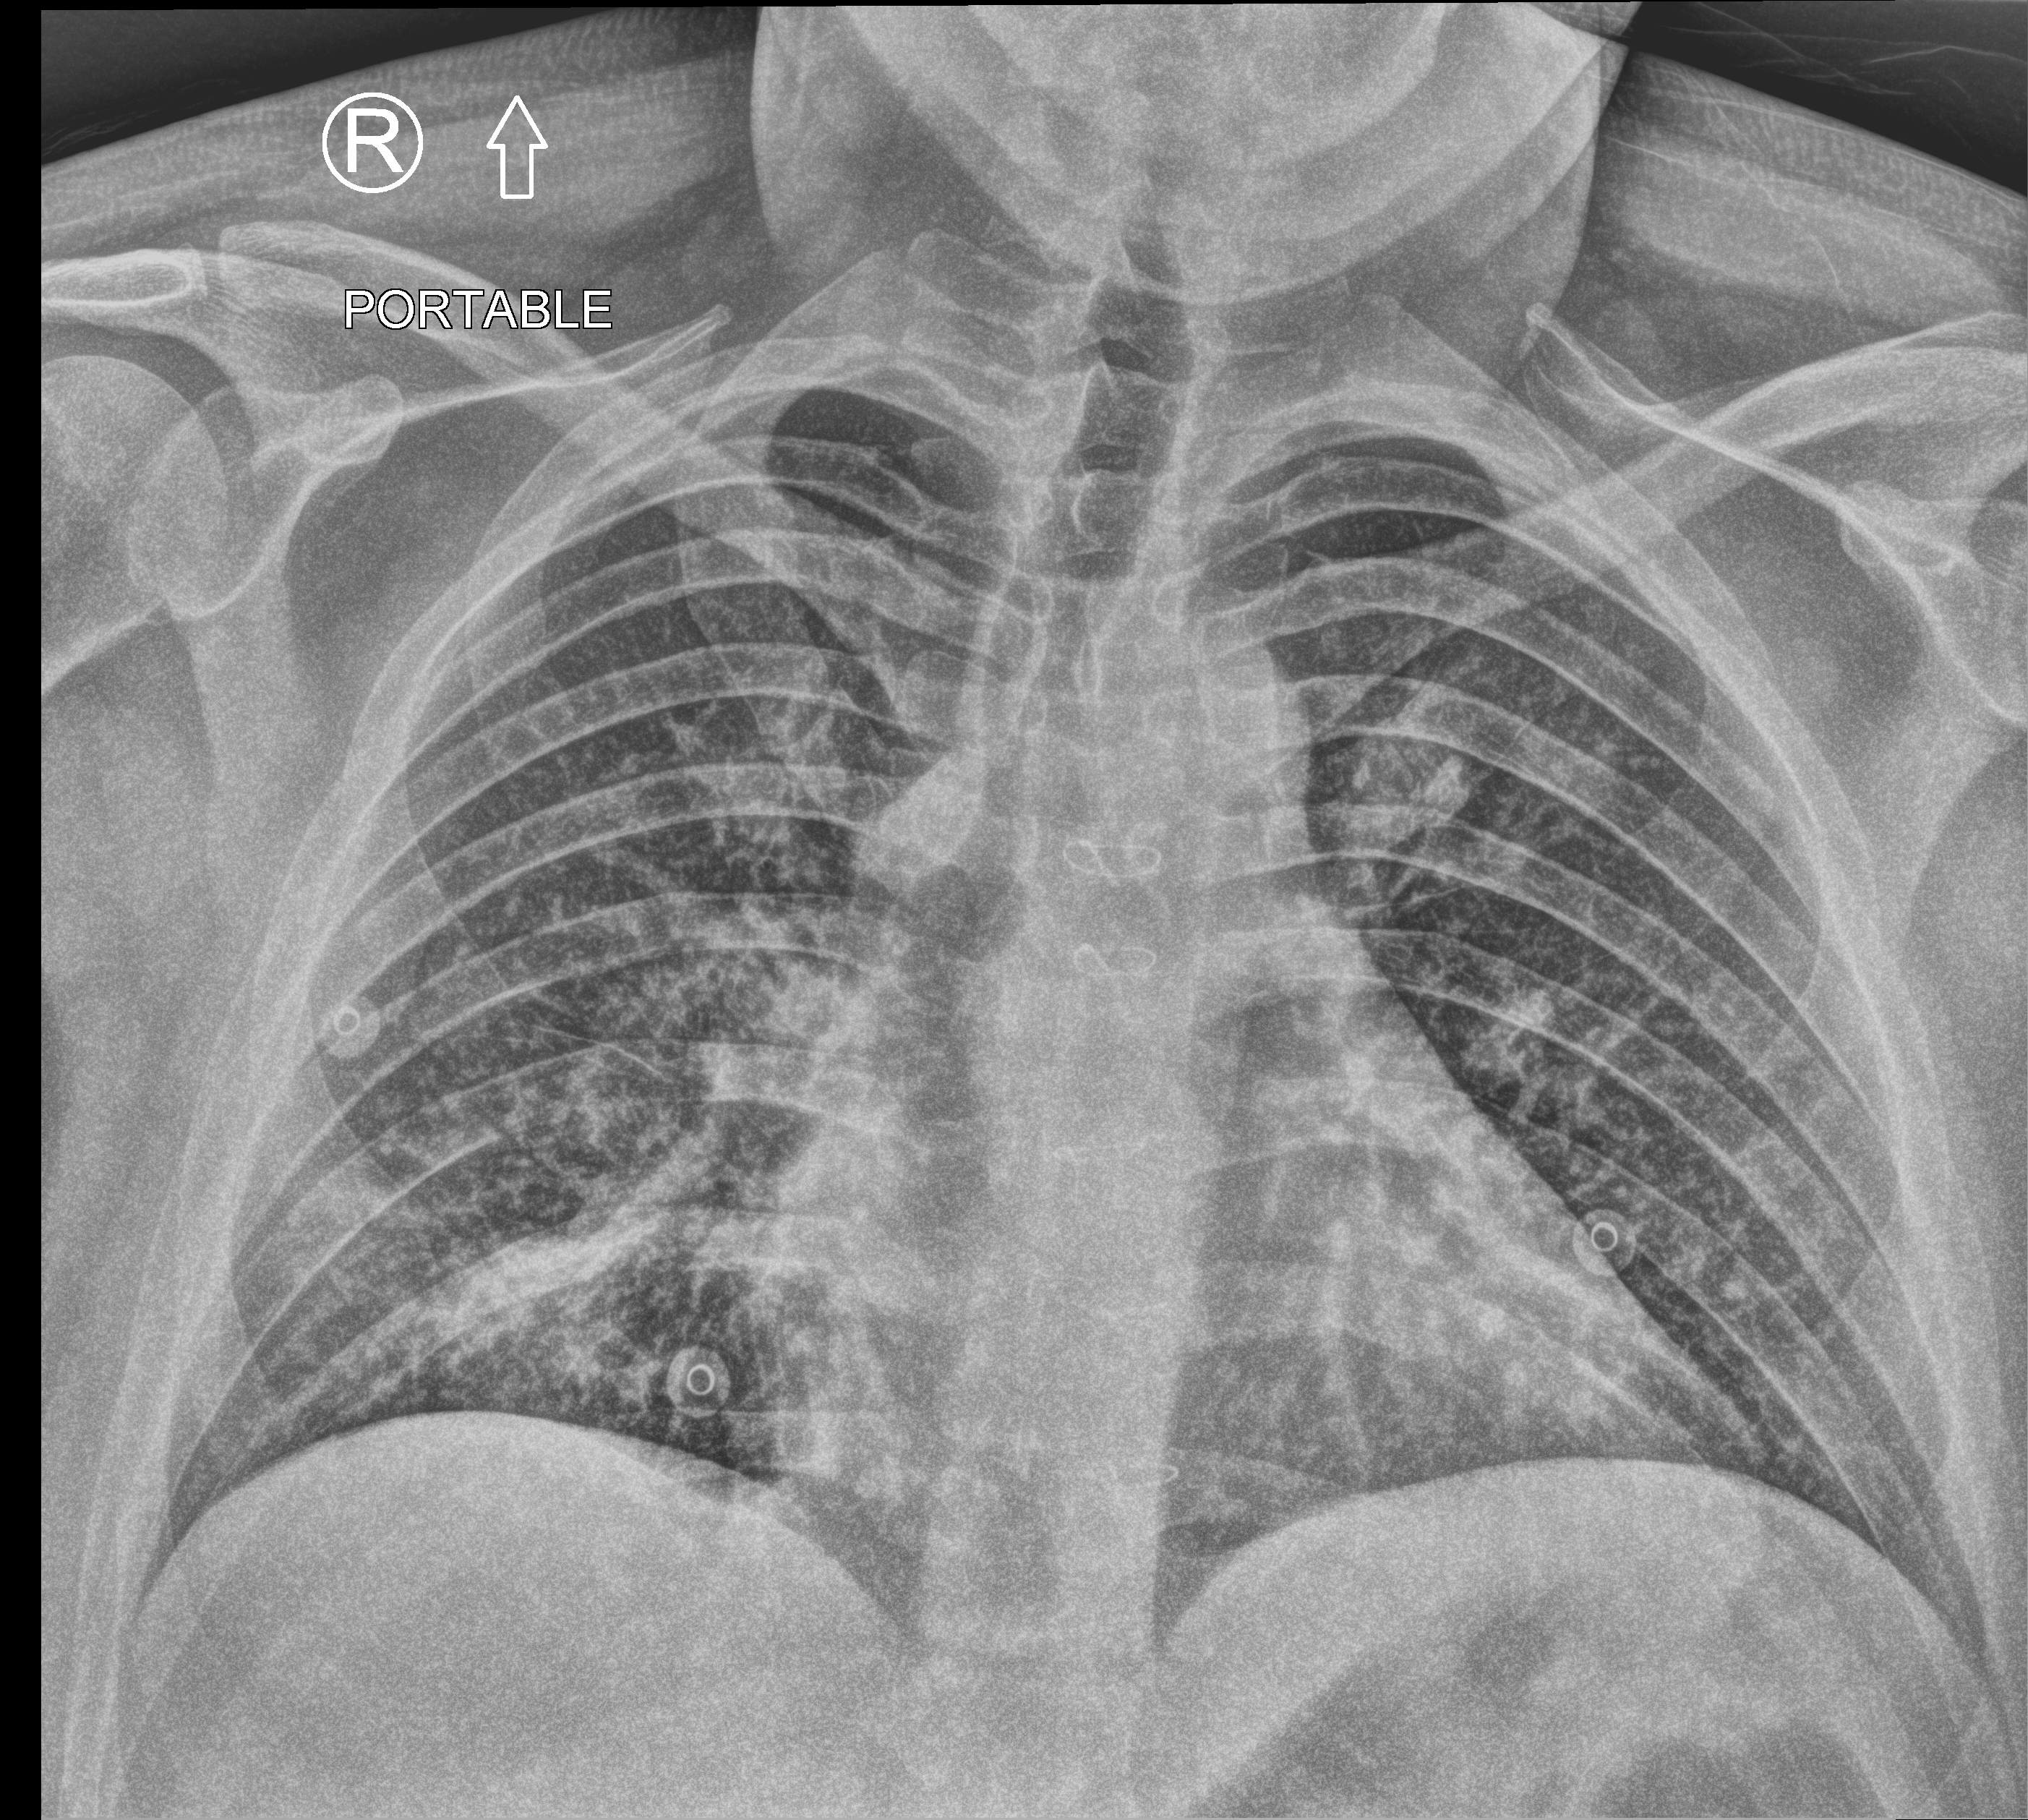
Chest X-ray (portable); anteroposterior (AP) projection. Patient hospitalised with COVID-19; male, aged 18–59 years.
Hospital-stay facts (about this admission, not read from this image; timing relative to this image not recorded): hypertension (admission record): no.